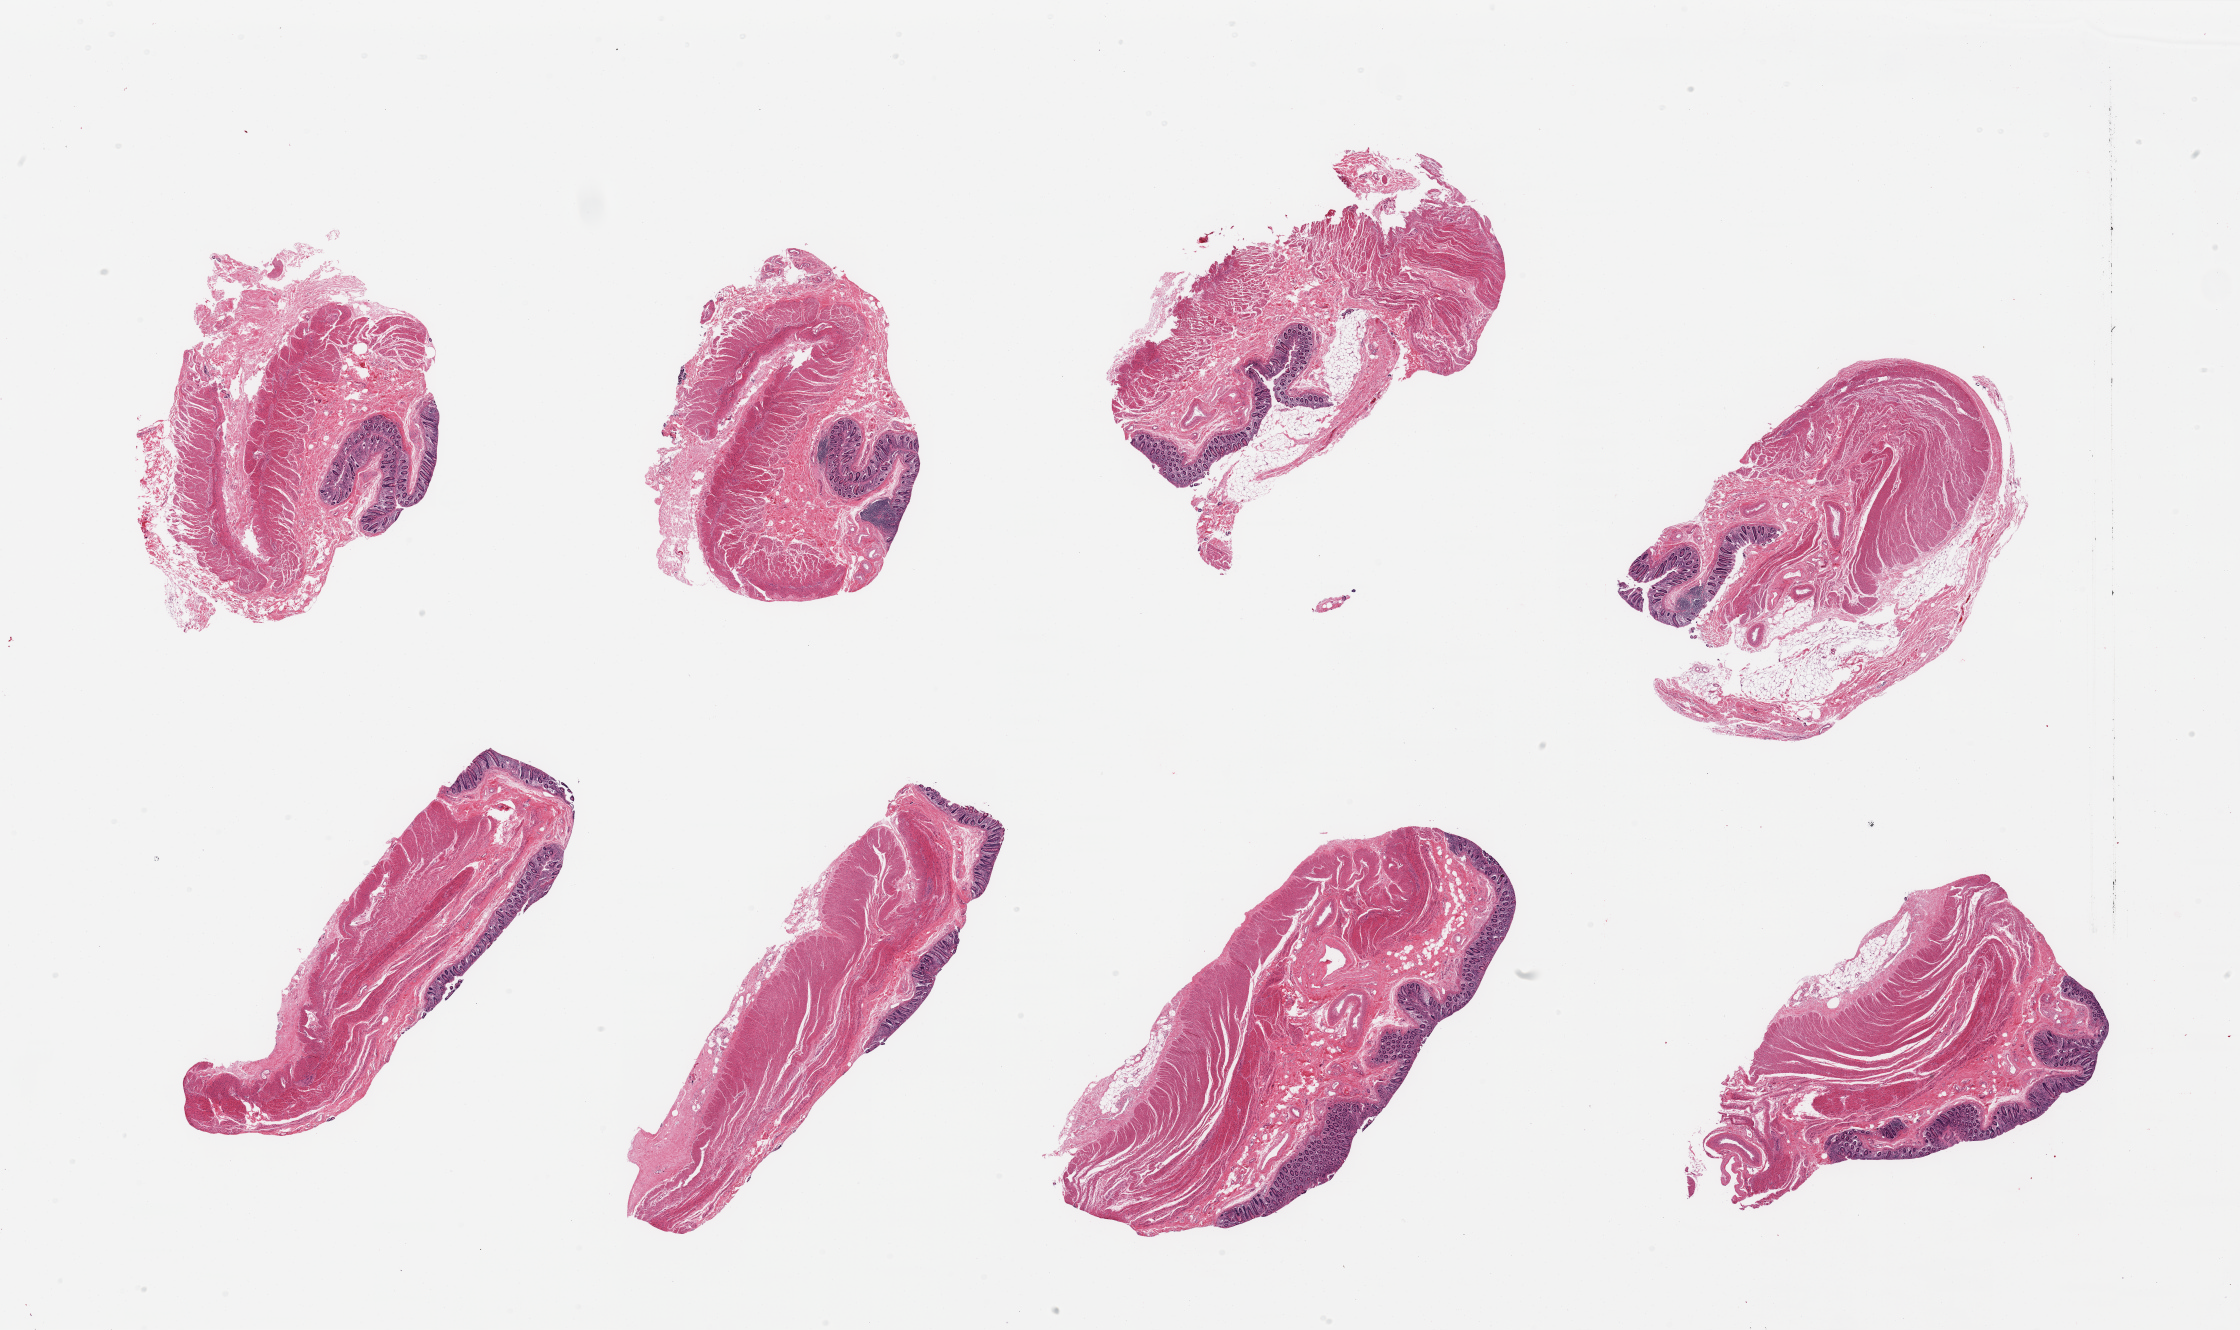
Whole-slide image, hematoxylin and eosin (H&E) stain, brightfield — a low-resolution overview of the entire scanned area, about 35.4 x 21.0 mm (slide scanned at 20x). PAXgene-fixed, paraffin-embedded tissue. Section of ileum (target tissue). Tissue donor sample. Donor sex: female.
• review note (as recorded): 8 pieces; mild to moderate autolysis of mucosa; very few lymphoid aggregates; submucosa and non target muscularis included